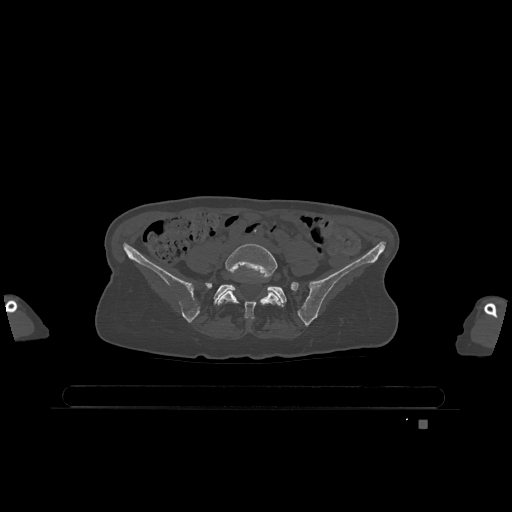
CT including the spine, one axial slice; slice 223 of 1317 in the series (ordered by position); bone window (W 1800 / L 400 HU); 0.5 mm slice thickness; 512 × 512 image matrix. Female patient, age 74 years. From the clinical record (not read from this slice): primary cancer: lung.
Outlined on this slice (semi-automatic segmentation, software-assisted and operator-edited):
- L5 vertebra: bounding box [x1, y1, x2, y2] px = [217, 244, 281, 320]